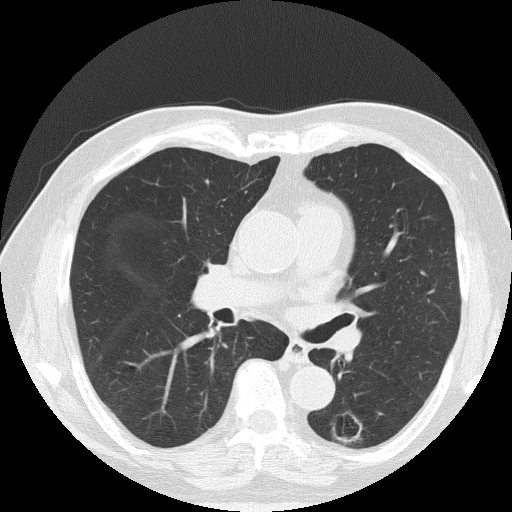
Axial slice from a low-dose chest CT screening exam. First (baseline) screen. Lung window (W 1500 / L -600 HU). 2 mm slice thickness. Lung (sharp) reconstruction kernel (FC51). 512 × 512 image matrix. Male, age 71 years at enrolment. Former smoker at enrolment.
- Lesion marked by an expert reader, bounding box <321,408,374,452> (left, top, right, bottom; pixels).
- No non-calcified nodule or mass ≥4 mm was recorded by the screening reader at this exam.
- Participant outcome: lung cancer diagnosed 340 days after this screen — adenocarcinoma, NOS, left lower lobe, poorly differentiated (G3), stage IA (AJCC 6th edition), 28 mm at pathology.